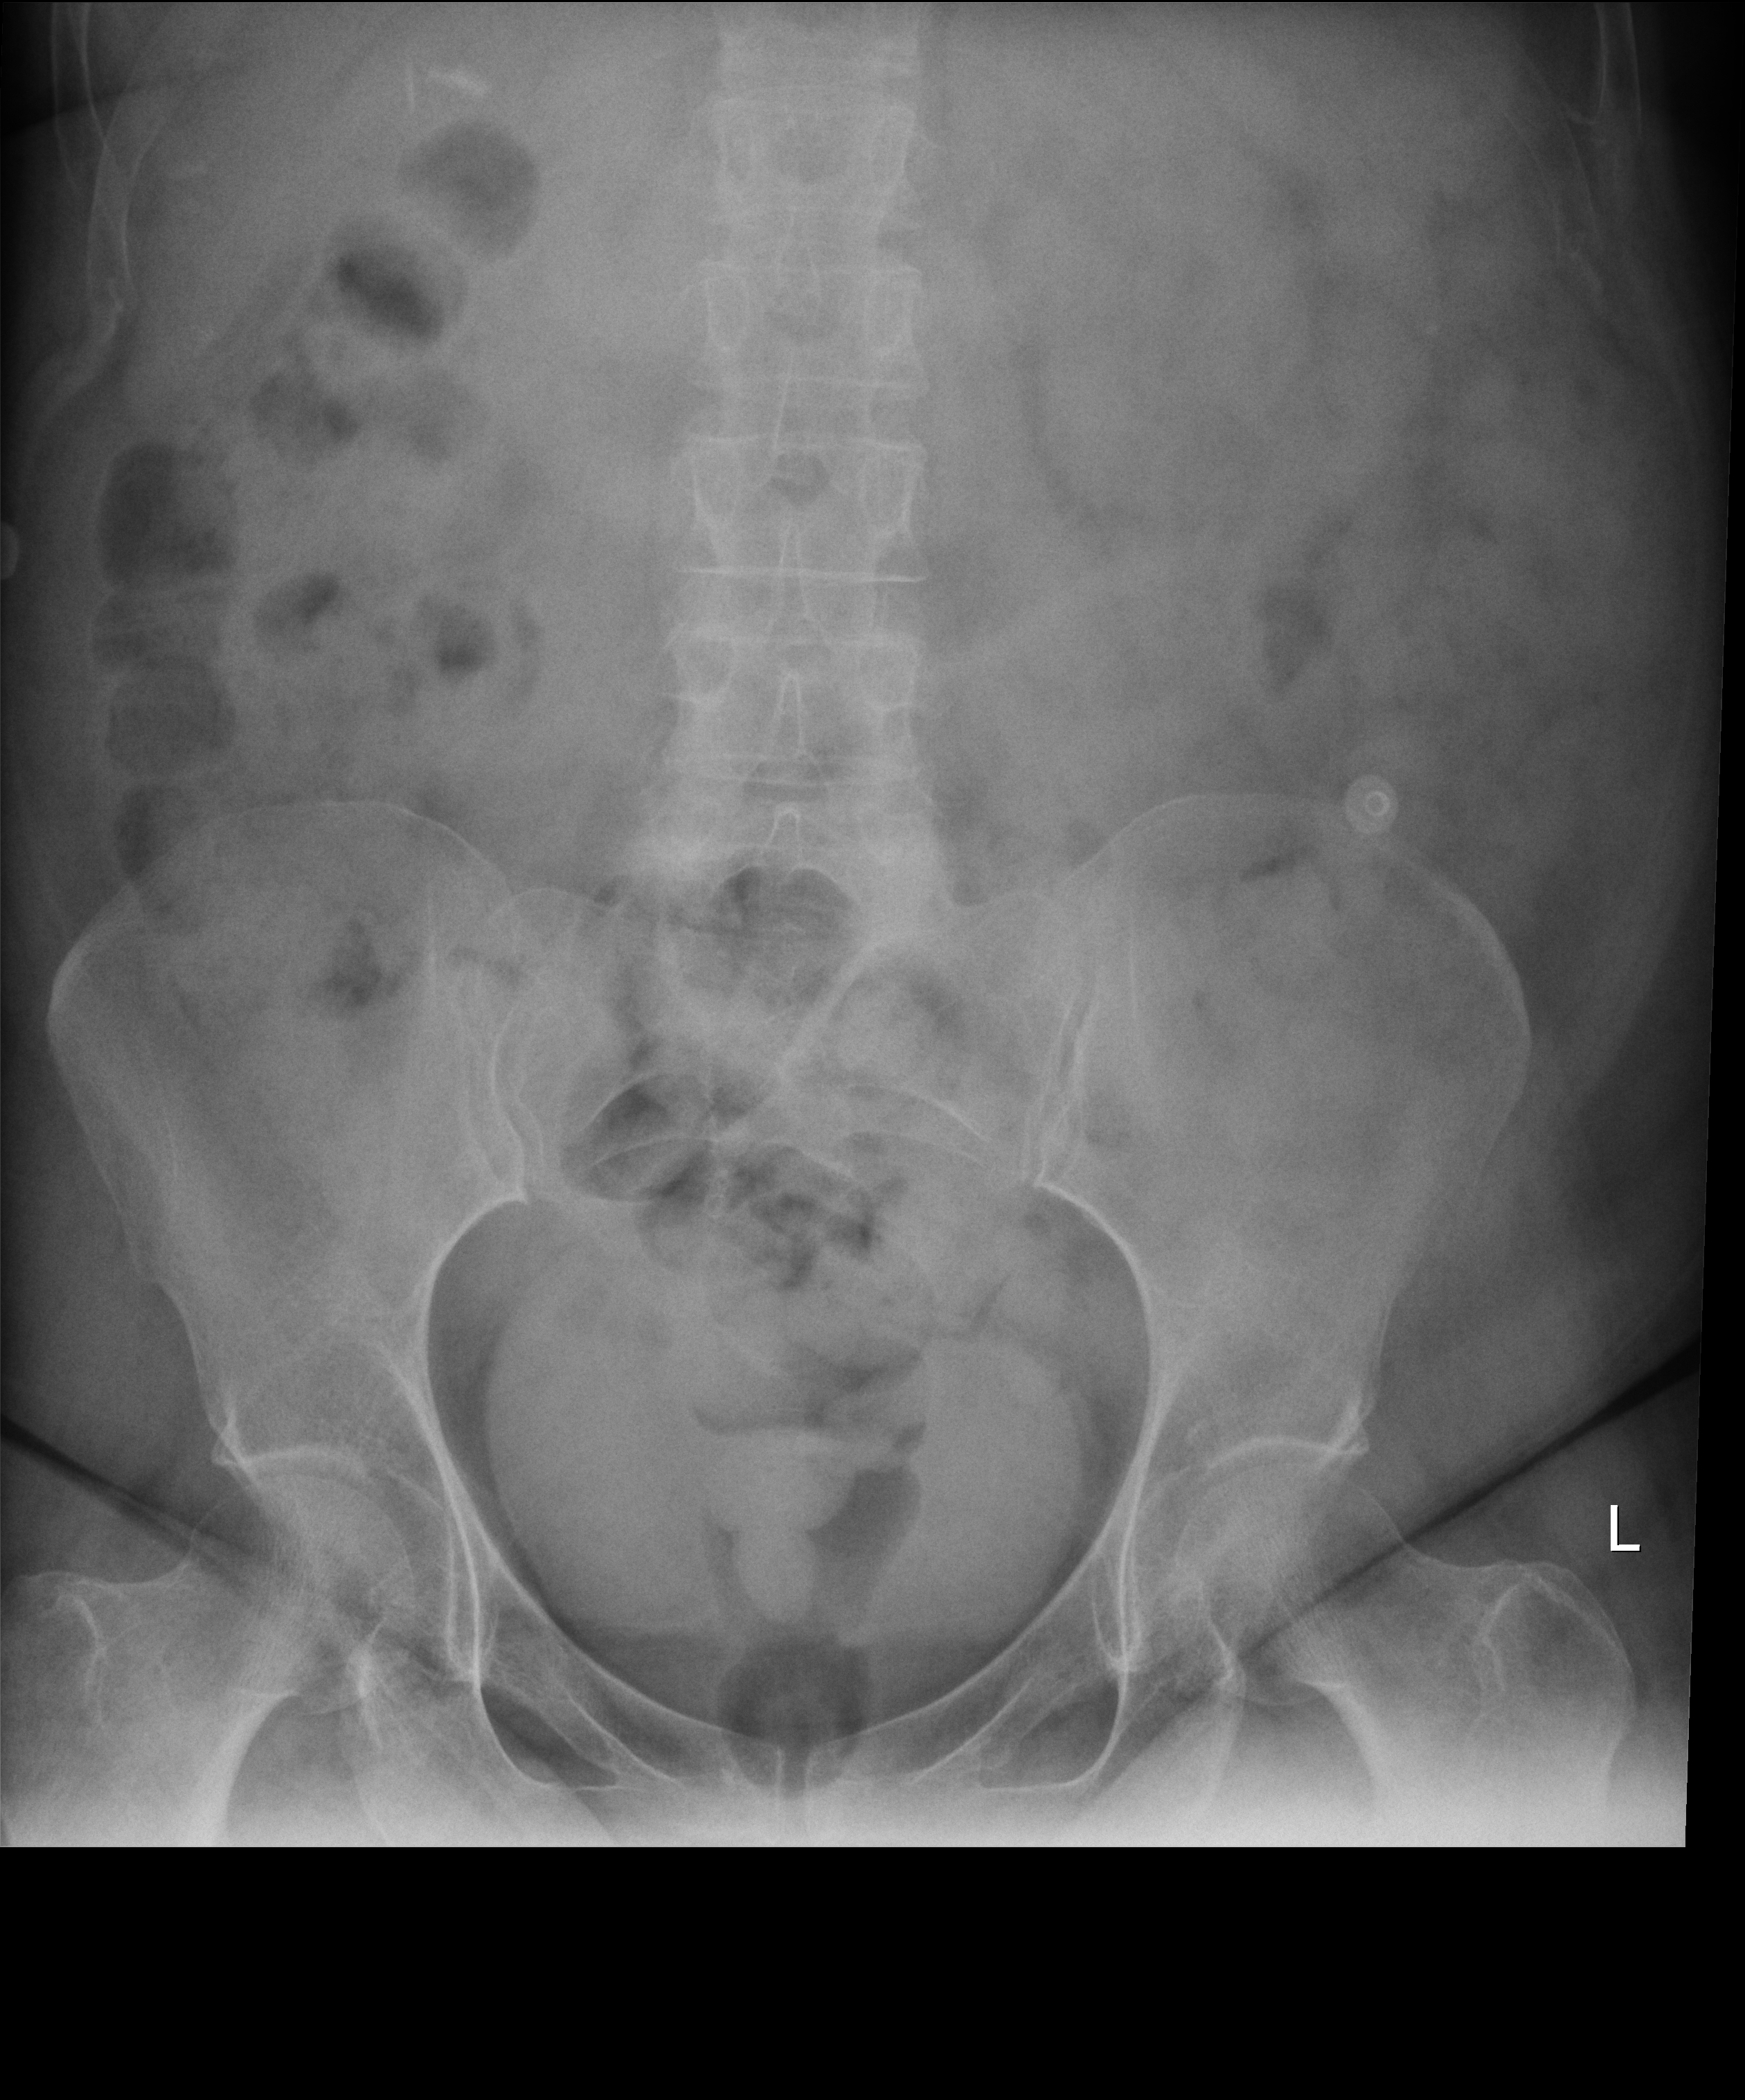
Abdomen X-ray (portable), anteroposterior (AP) projection. Female patient hospitalised with COVID-19, age 18–59 years.
From the hospital-stay record, not from the radiograph (when in the stay this image was taken is not recorded):
- mechanically ventilated during this hospital stay: no